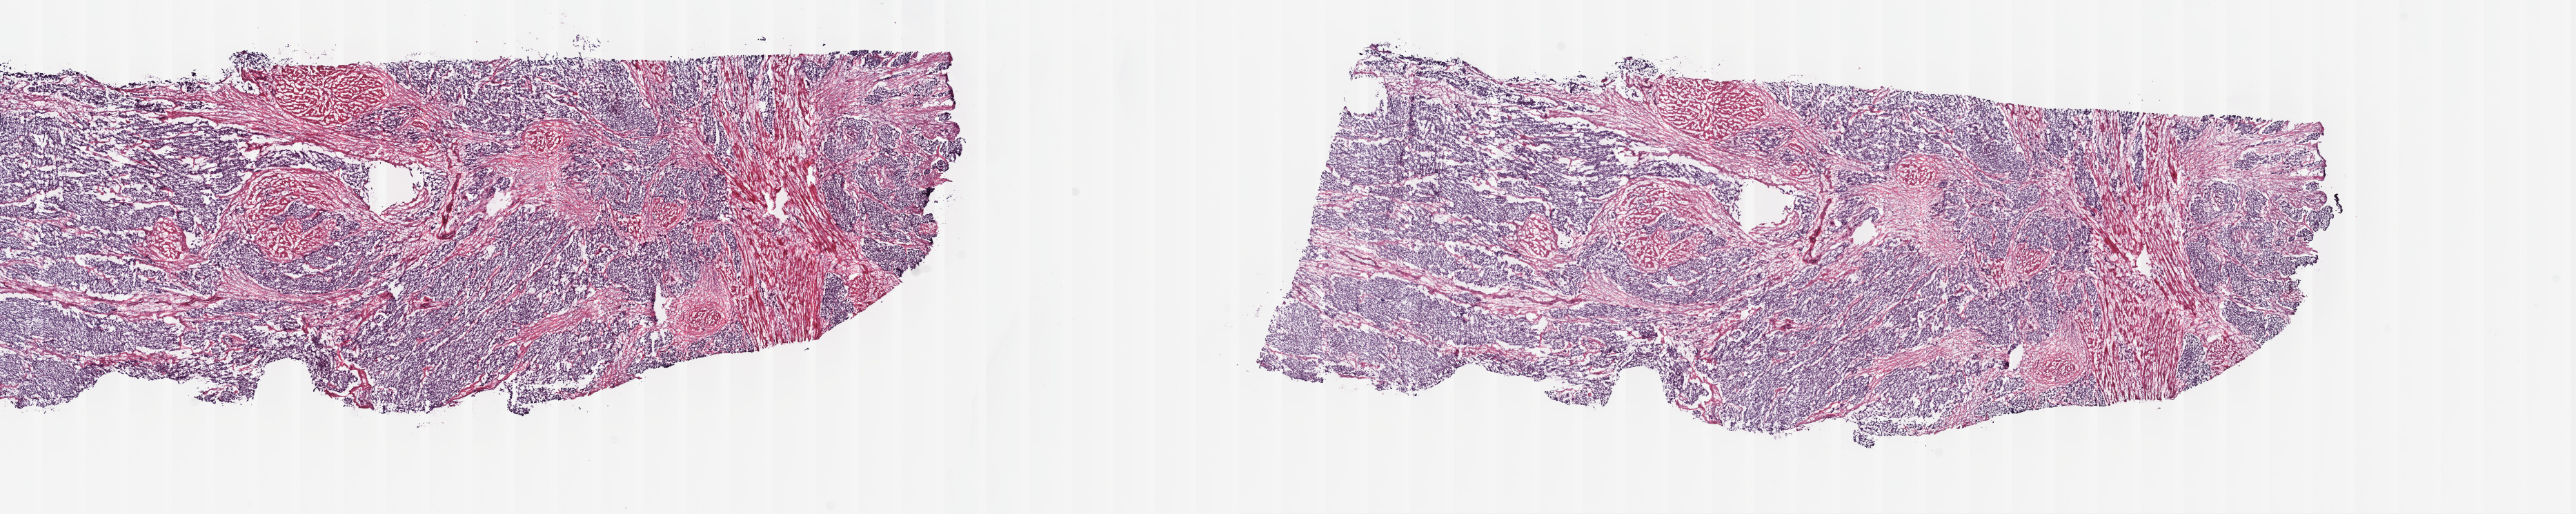
H&E whole-slide image — shown as a low-resolution overview of the whole scanned area (about 30.2 x 6.0 mm, slide scanned at 40x), frozen section from the top of the tissue portion, bladder, primary tumour sample. Male patient; age at initial diagnosis 79 years. Histologic grade: high grade. Pathologist review of this section (percent, as recorded): tumour cells 70%, tumour nuclei 70%, normal cells 0%, stromal cells 27%, necrosis 3%. Inflammatory infiltration, as recorded: lymphocyte infiltration 3%, monocyte infiltration 2%, neutrophil infiltration 5%.
• AJCC pathologic stage: IV (6th edition)
• lymph nodes positive (case pathology): 1 of 15 examined
• histologic diagnosis: Transitional cell carcinoma